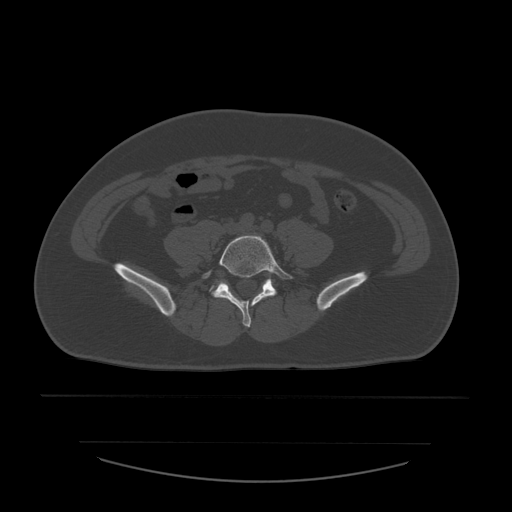
CT including the spine, one axial slice. Position 119 of 532 along the scan axis. Reconstruction kernel STANDARD. Bone window (W 1800 / L 400 HU). 1.25 mm slice thickness. 512 × 512 image matrix, field of view 441 × 441 mm. Patient age 44 years. From the clinical record (not read from this slice): primary cancer: soft tissue sarcoma.
Structures marked on this image (semi-automatically segmented with operator editing):
- L5 vertebra: bounding box (x1, y1, x2, y2) in pixels: (203, 233, 294, 328)